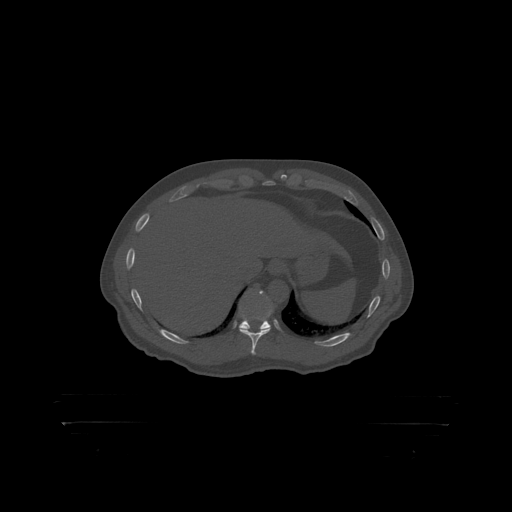
CT including the spine, one axial slice. Slice 392 of 399 in the series (ordered by position). Bone window (W 1800 / L 400 HU). 1.25 mm slice thickness. 512 × 512 image matrix. Patient: male, 46 years. From the clinical record (not read from this slice): primary cancer: skin.
Outlined on this slice (semi-automatic segmentation, software-assisted and operator-edited):
- T10 vertebra: bounding box <240,292,273,319> (left, top, right, bottom; pixels)
- T11 vertebra: <243,296,264,319>